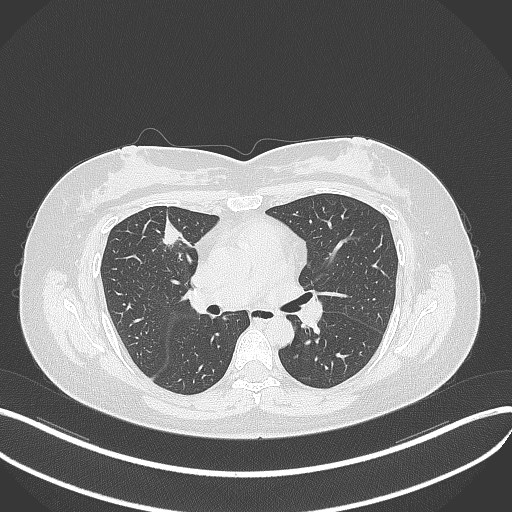
Chest CT, one axial slice; position 181 of 273 along the scan axis; reconstruction kernel B70f; lung window (W 1500 / L -600 HU); 1 mm slice thickness; 512 × 512 image matrix. Patient: female, 42 years. Case-level facts recorded for this patient, not image findings: clinical TNM (as recorded): T1b N0 M0.
Structures marked on this image (bounding box drawn by a radiologist):
- lung tumour (recorded histology: adenocarcinoma): bounding box <157,216,183,252> (left, top, right, bottom; pixels)